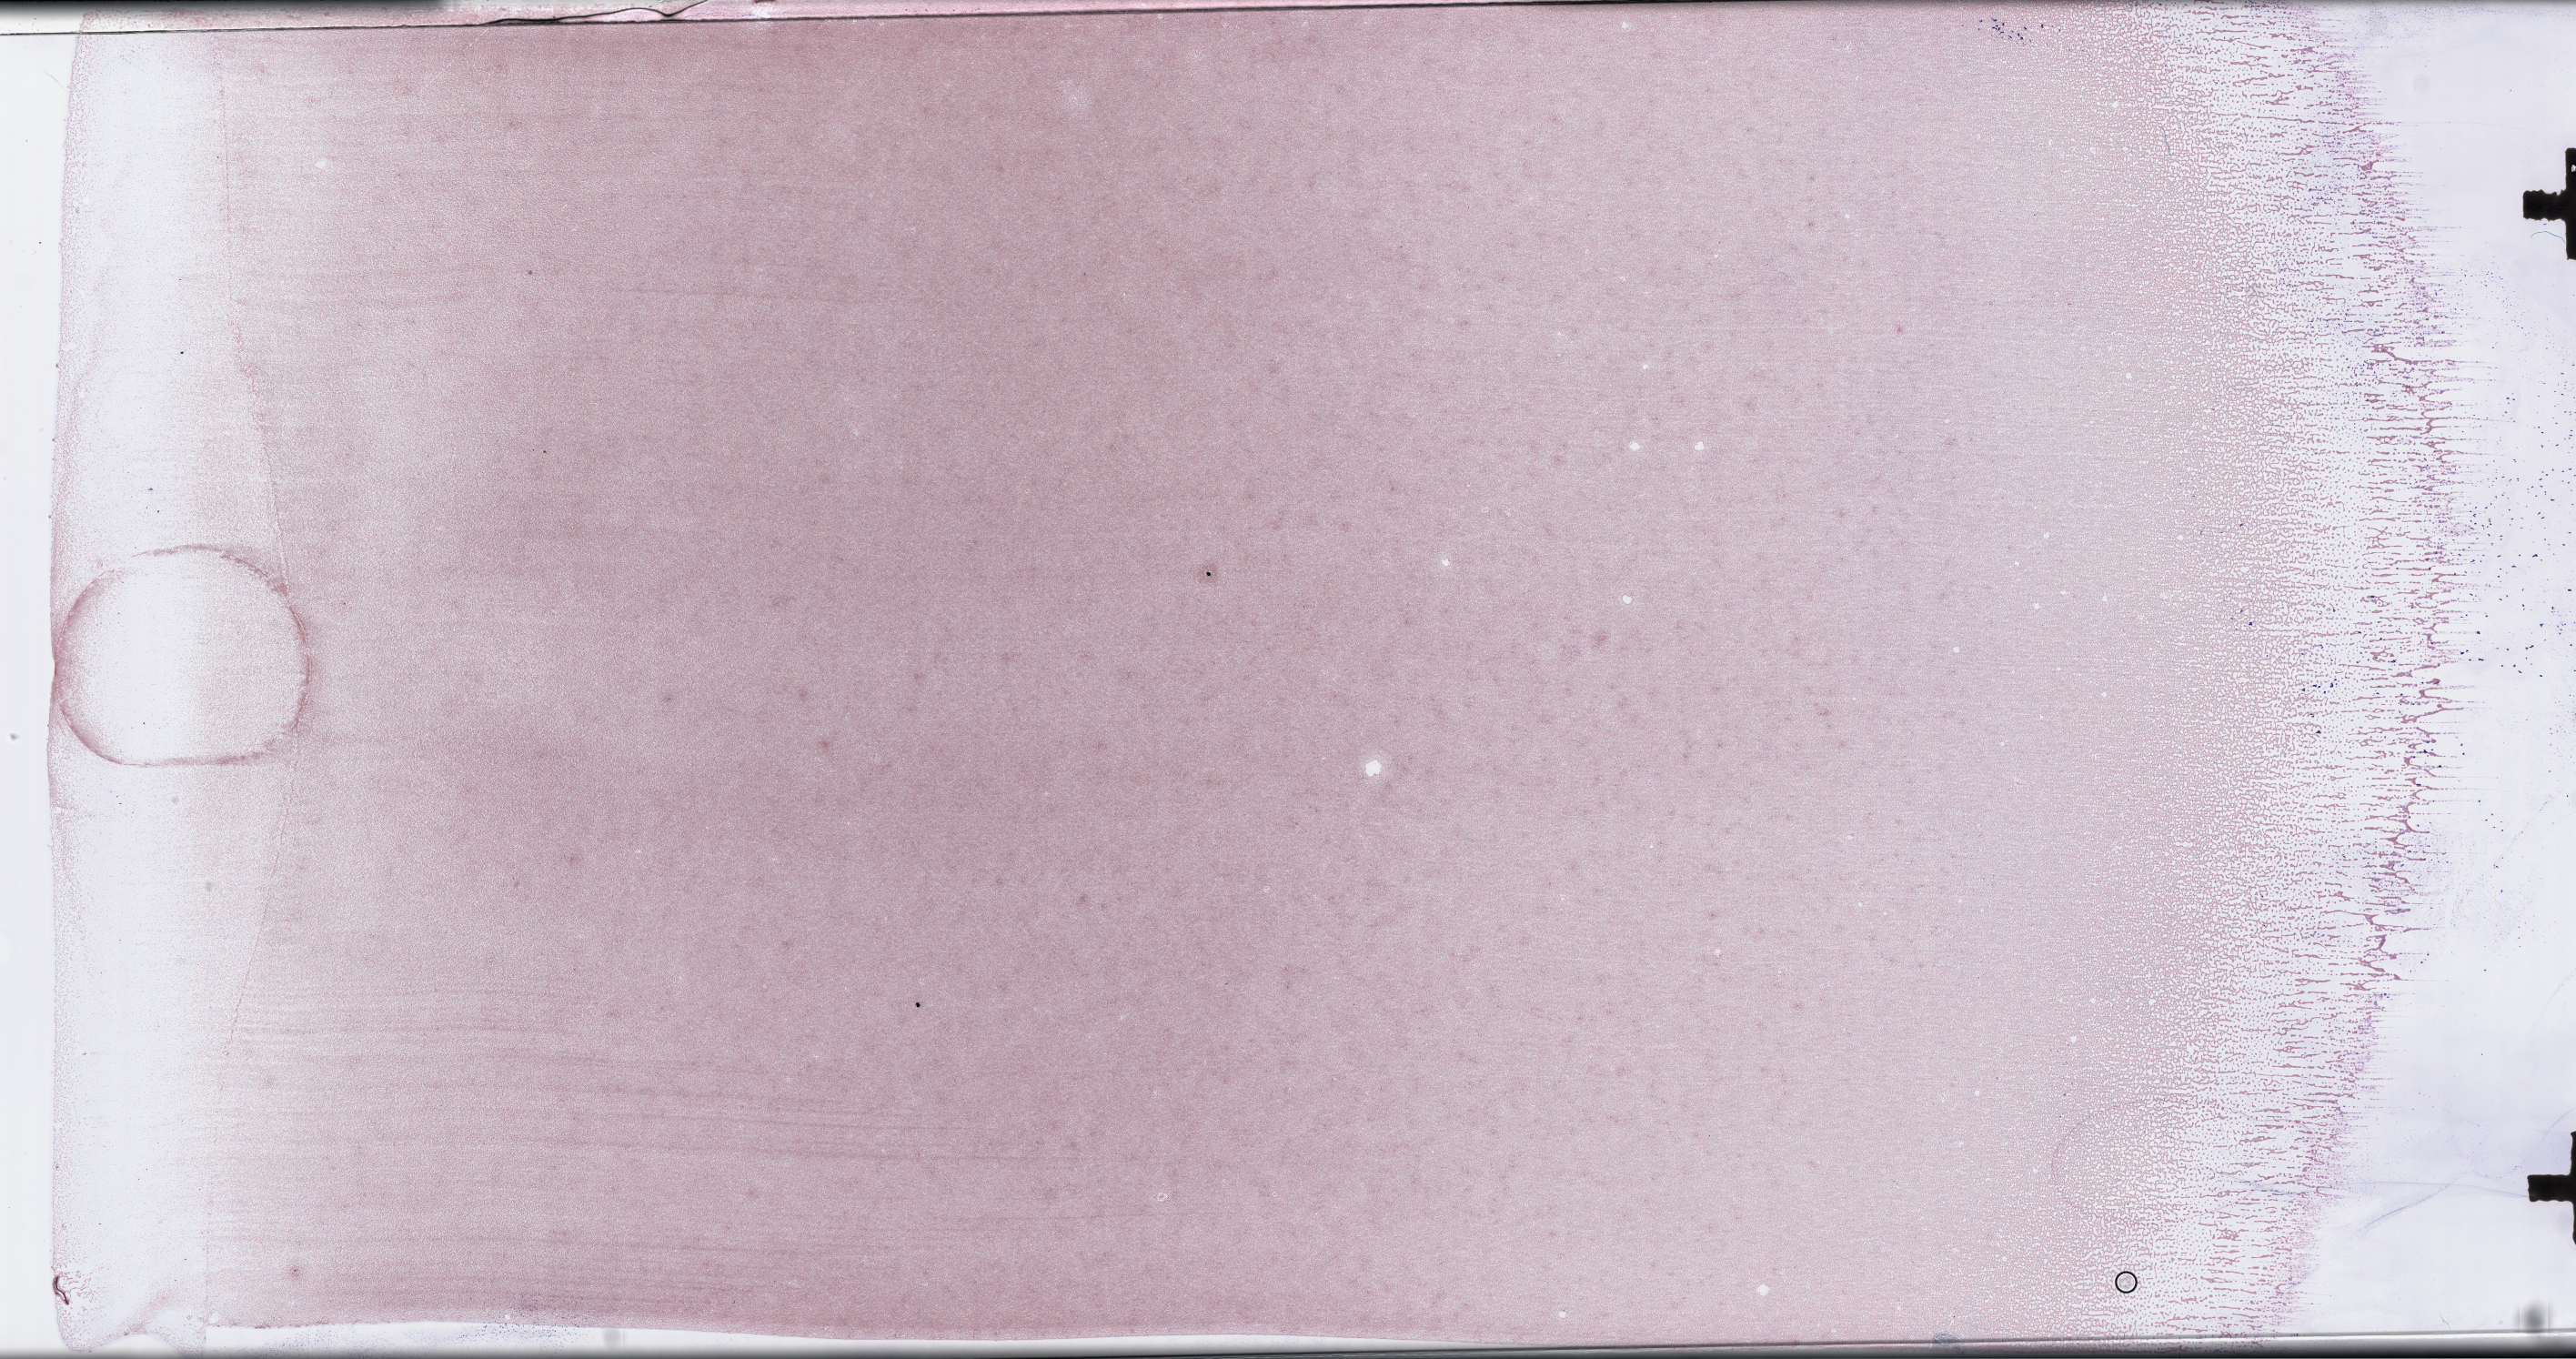
Wright–Giemsa-stained bone marrow smear, whole-slide image, low-resolution overview of the scanned area, about 45.7 x 24.1 mm, smear from an EDTA sample, collected at baseline (before treatment). Patient: female.
Patient diagnosis: Plasma Cell Myeloma.